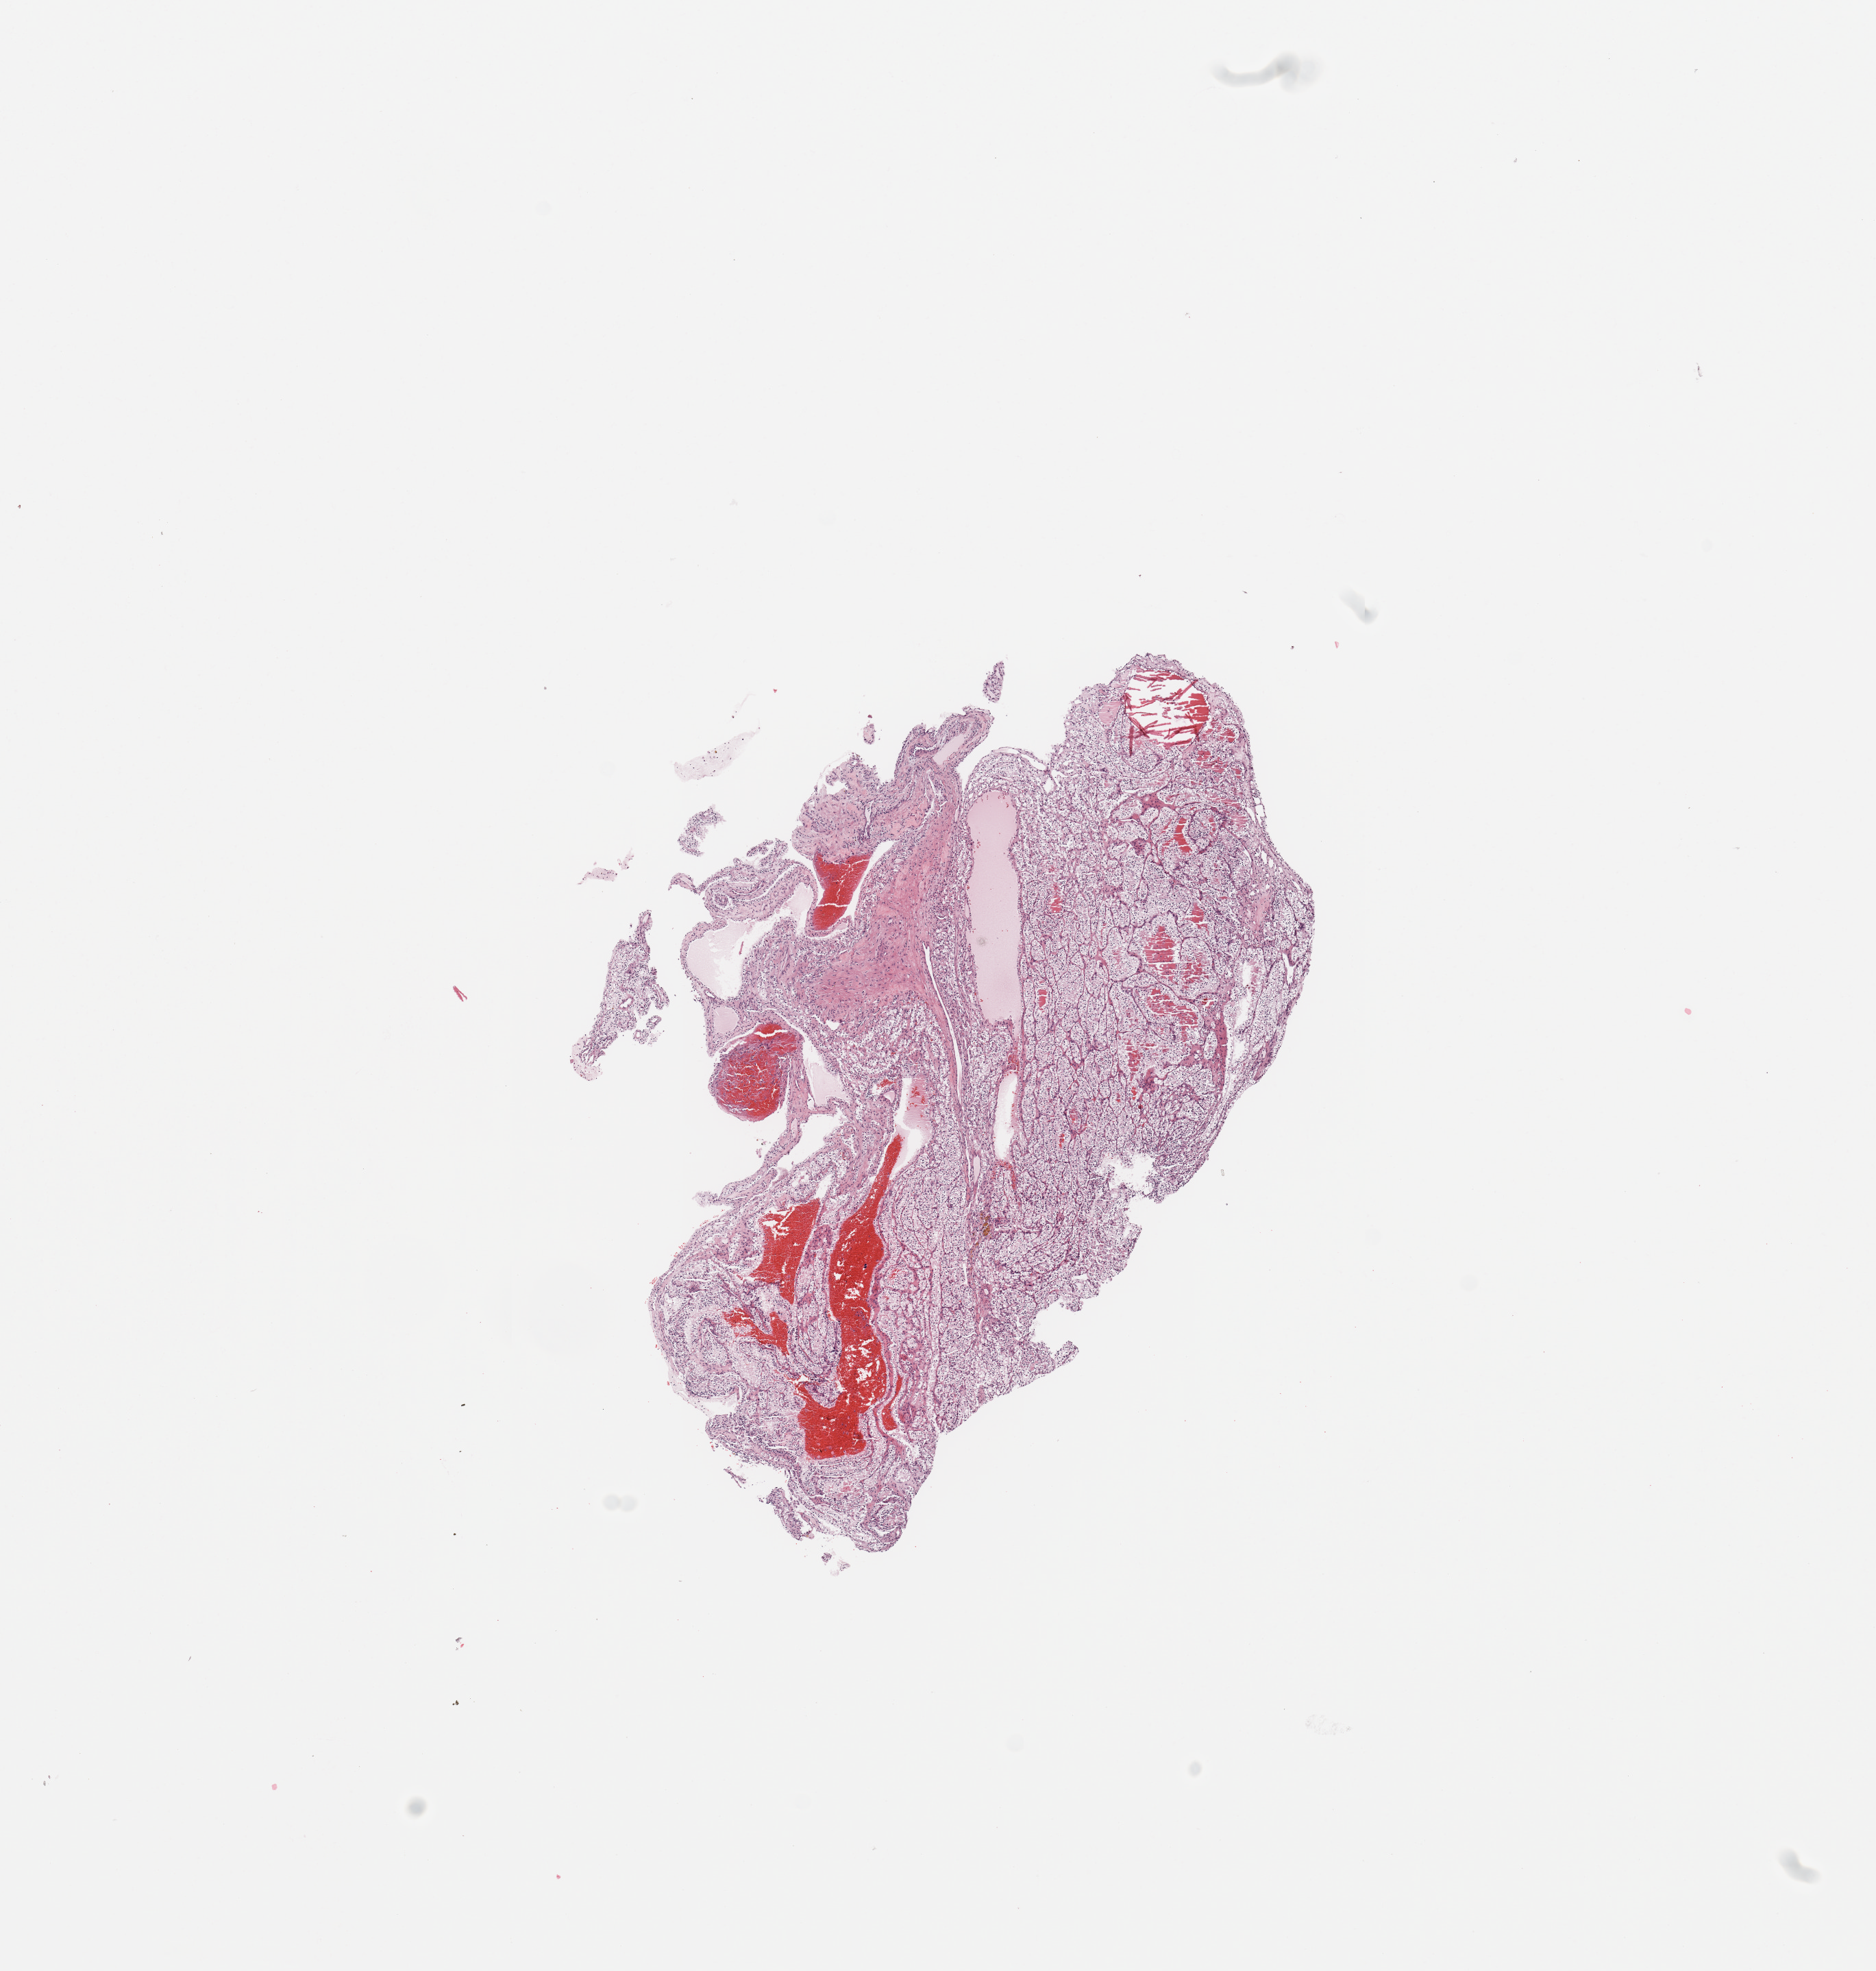
H&E-stained whole-slide image, low-resolution overview of the scanned area, about 10.8 x 11.4 mm (acquisition: 20x scan), tumour tissue sample, sampled site: kidney. Female, 56 y/o. Histologic grade: G1 (well differentiated). Slide review estimates, as recorded: tumour nuclei 85%, necrosis 3%.
- diagnosis: Renal cell carcinoma, NOS
- primary tumour site (as recorded): middle
- AJCC pathologic stage: I